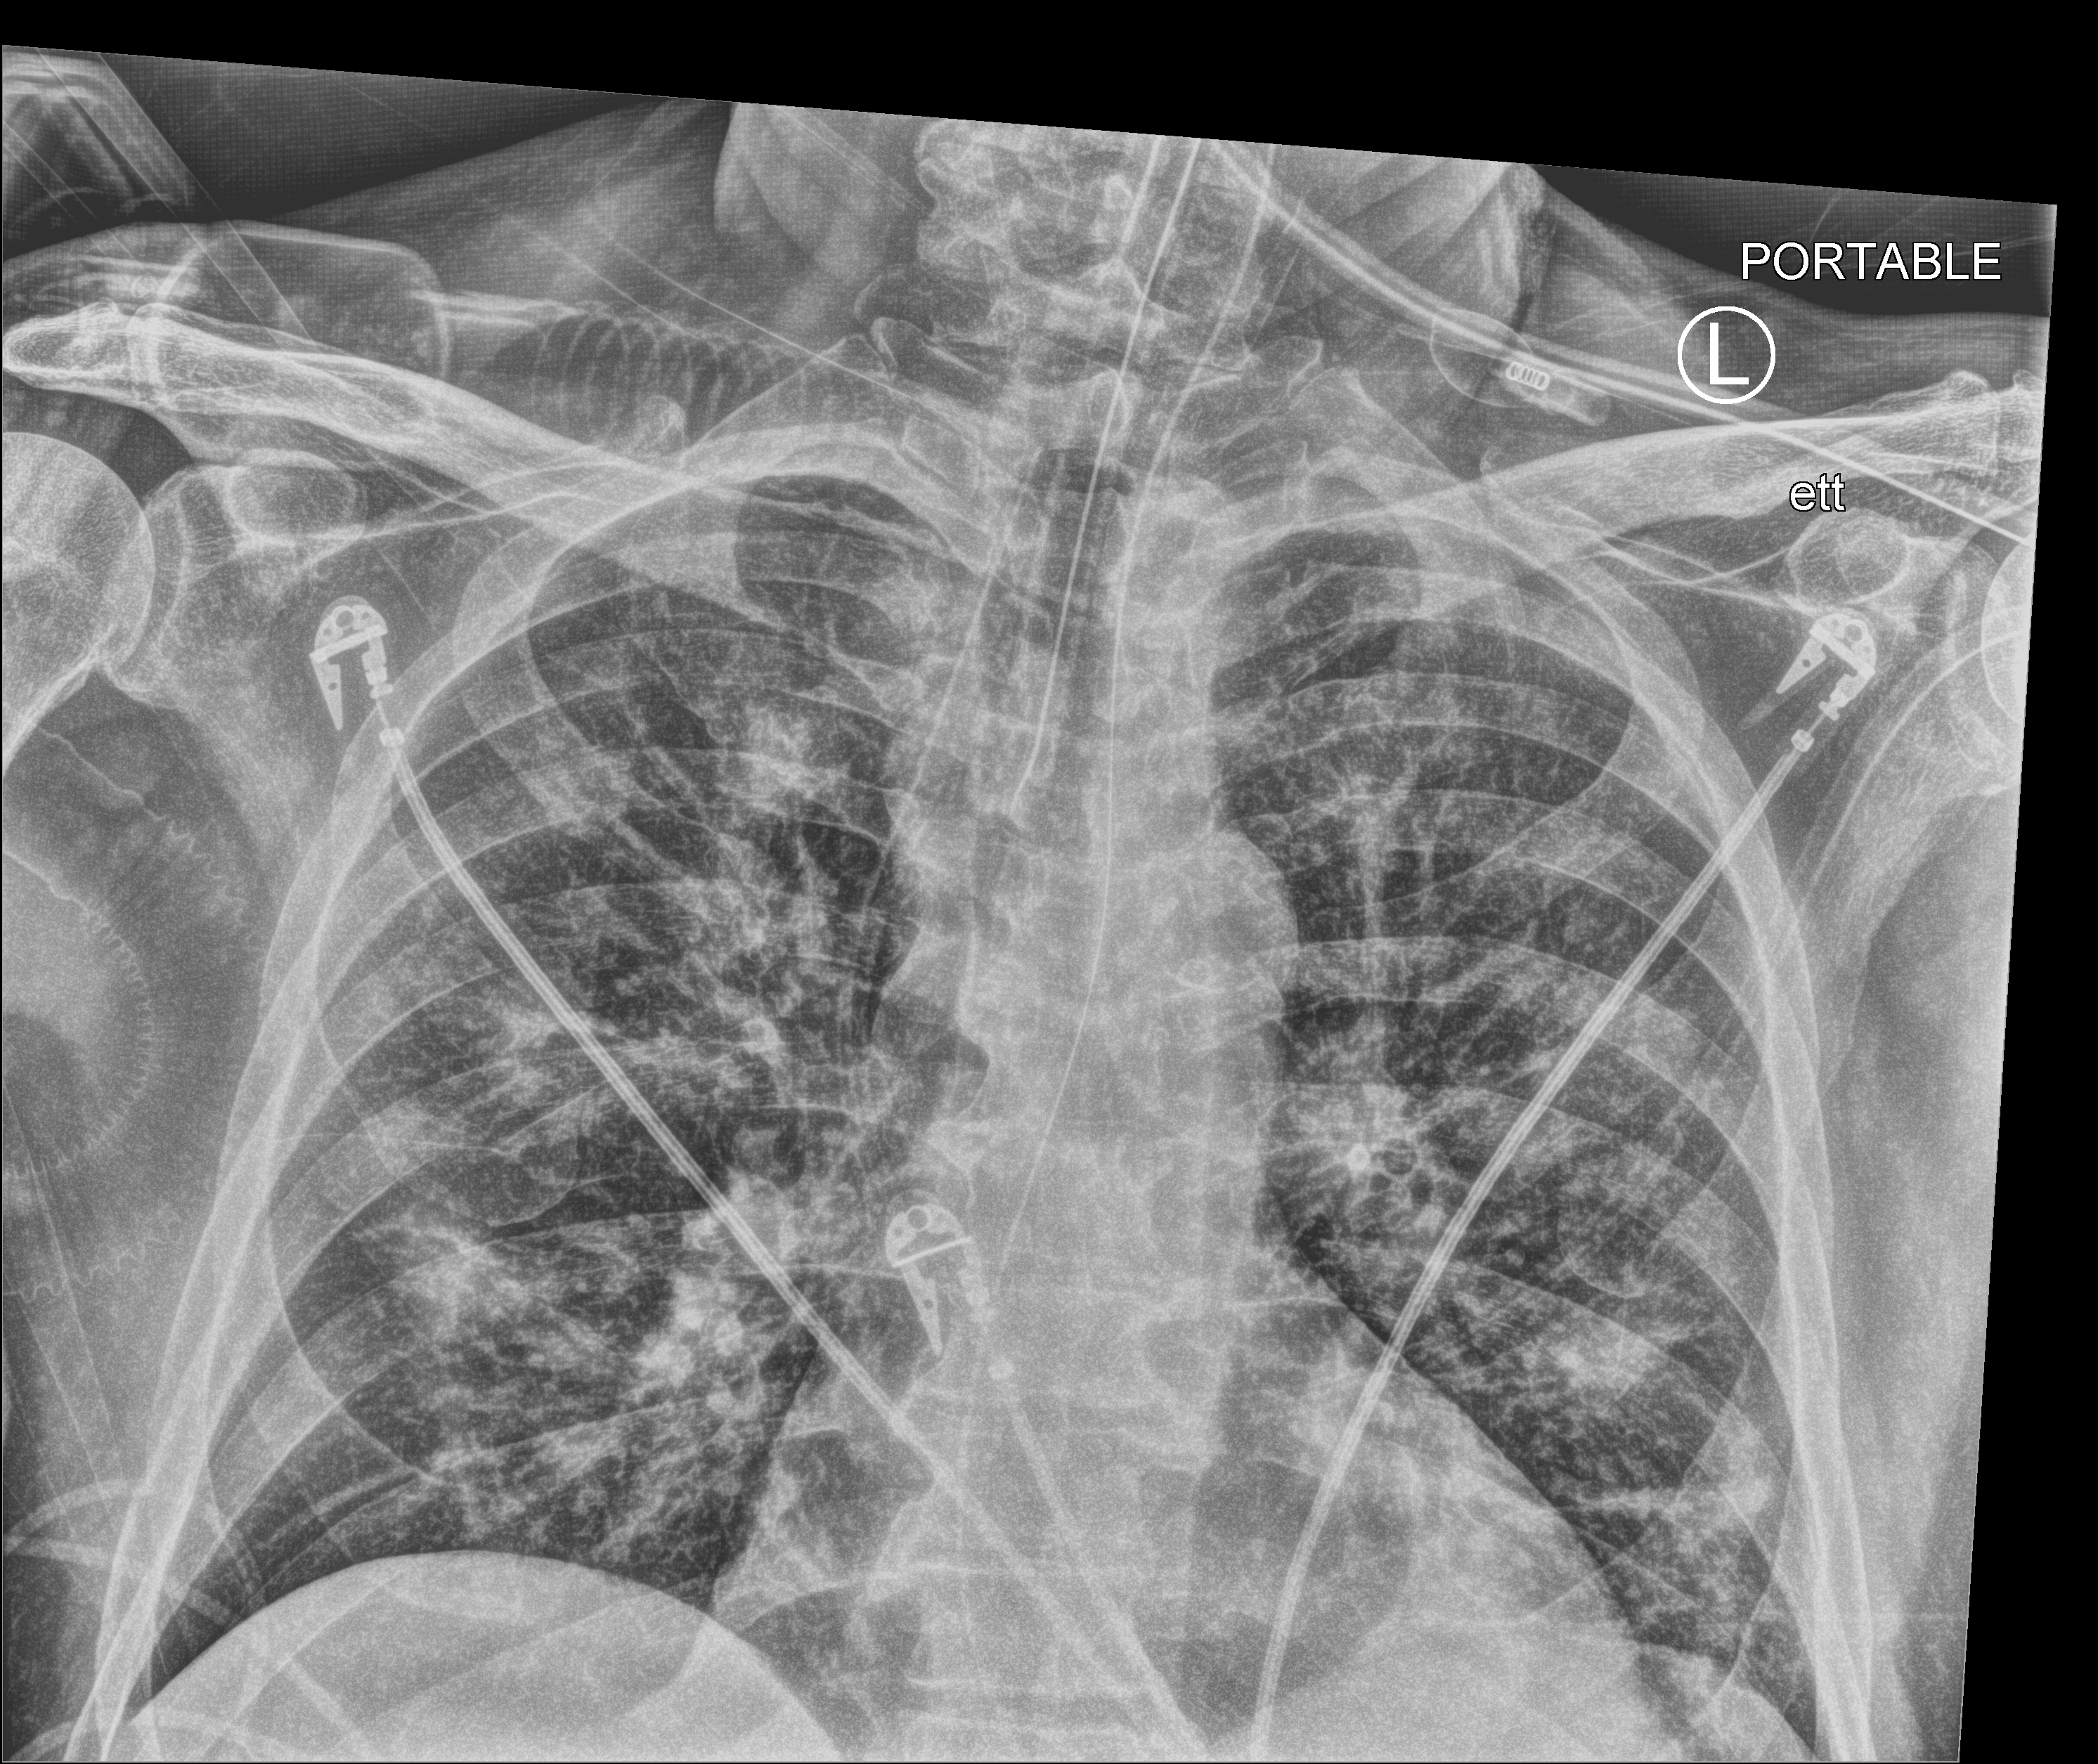
Portable chest radiograph; anteroposterior (AP) projection. Patient hospitalised with COVID-19; male, aged 60–74 years.
Hospital-stay facts (about this admission, not read from this image; timing relative to this image not recorded):
- mechanically ventilated during this hospital stay: yes
- length of hospital stay: 35 days
- other chronic lung disease (admission record): no